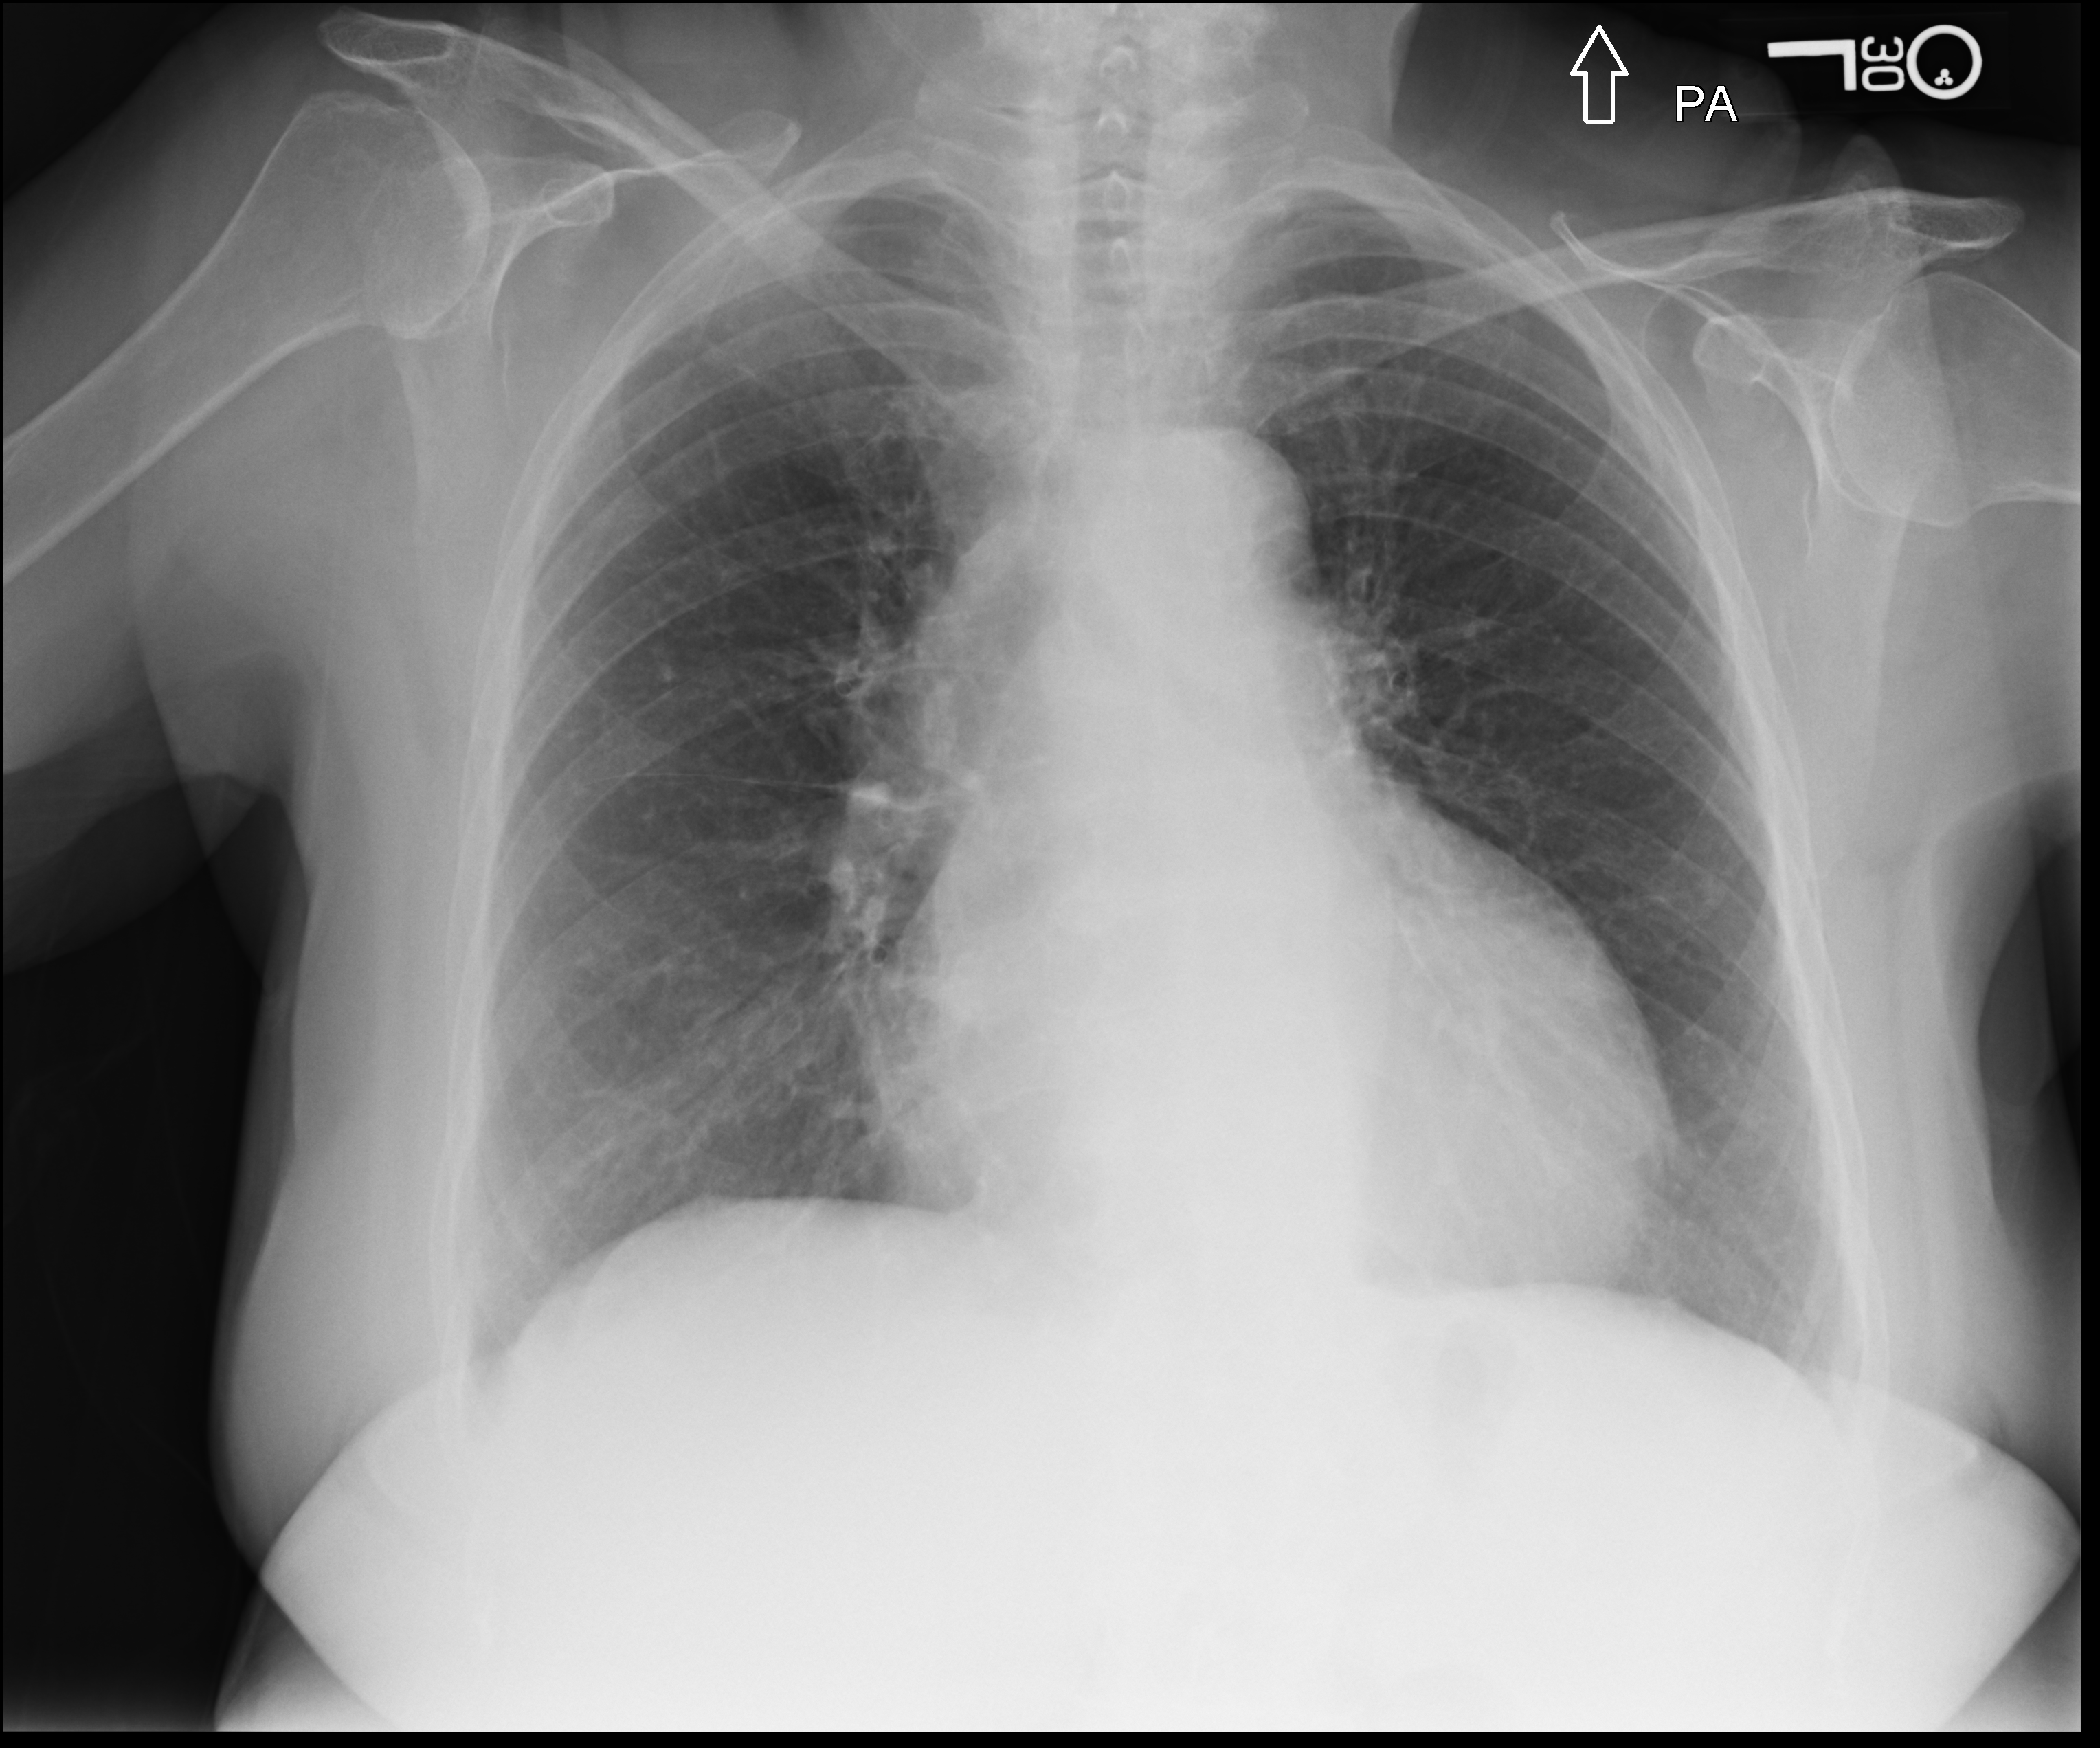
Chest radiograph (computed radiography), posteroanterior (PA) projection. Female patient hospitalised with COVID-19, age 75–90 years.
From the hospital-stay record, not from the radiograph (when in the stay this image was taken is not recorded): mechanically ventilated during this hospital stay: no.